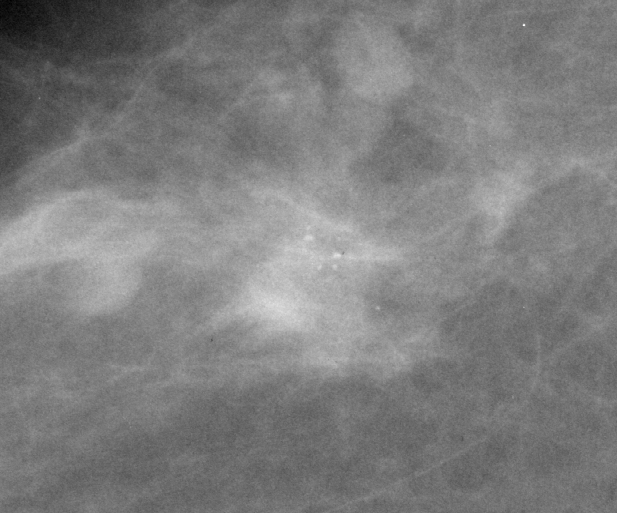
Cropped region of a digitized screen-film mammogram centred on a radiologist-marked abnormality; right breast; CC view.
- Finding: calcifications, morphology pleomorphic, distribution clustered; BI-RADS assessment category 5; subtlety rating 4 on a 1 (subtle) to 5 (obvious) scale; pathology result (as recorded, not read from the image): malignant.